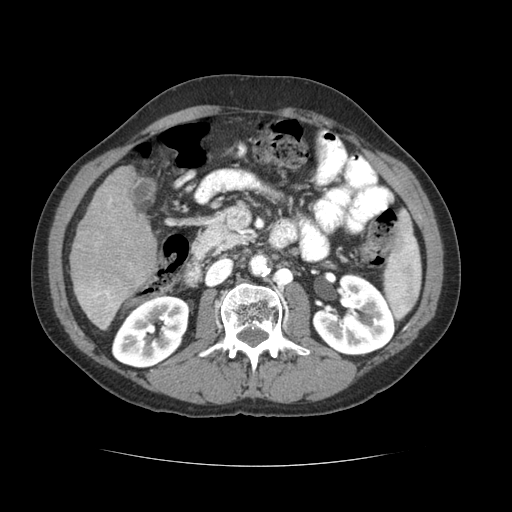
Contrast-enhanced abdominal CT (liver protocol), one axial slice. Position 23 of 69 along the scan axis. Reconstruction kernel STANDARD. Soft-tissue window (W 400 / L 40 HU). 2.5 mm slice thickness. 512 × 512 image matrix, field of view 360 × 360 mm. Case-level facts recorded for this patient, not image findings: diagnosis: hepatocellular carcinoma (patient treated with transarterial chemoembolisation; whether this scan precedes or follows treatment is not stated here); TNM stage (as recorded): Stage-II; Child-Pugh class: B; tumour differentiation: poorly differentiated; tumour nodularity: multinodular.
Outlined on this slice (semi-automatically segmented with operator editing):
- liver parenchyma outside the tumour (the mass and vessels are separate outlines, so this box may not span the whole liver): bounding box (x1, y1, x2, y2) in pixels: (70, 166, 156, 329)
- liver vessels: (77, 198, 120, 328)